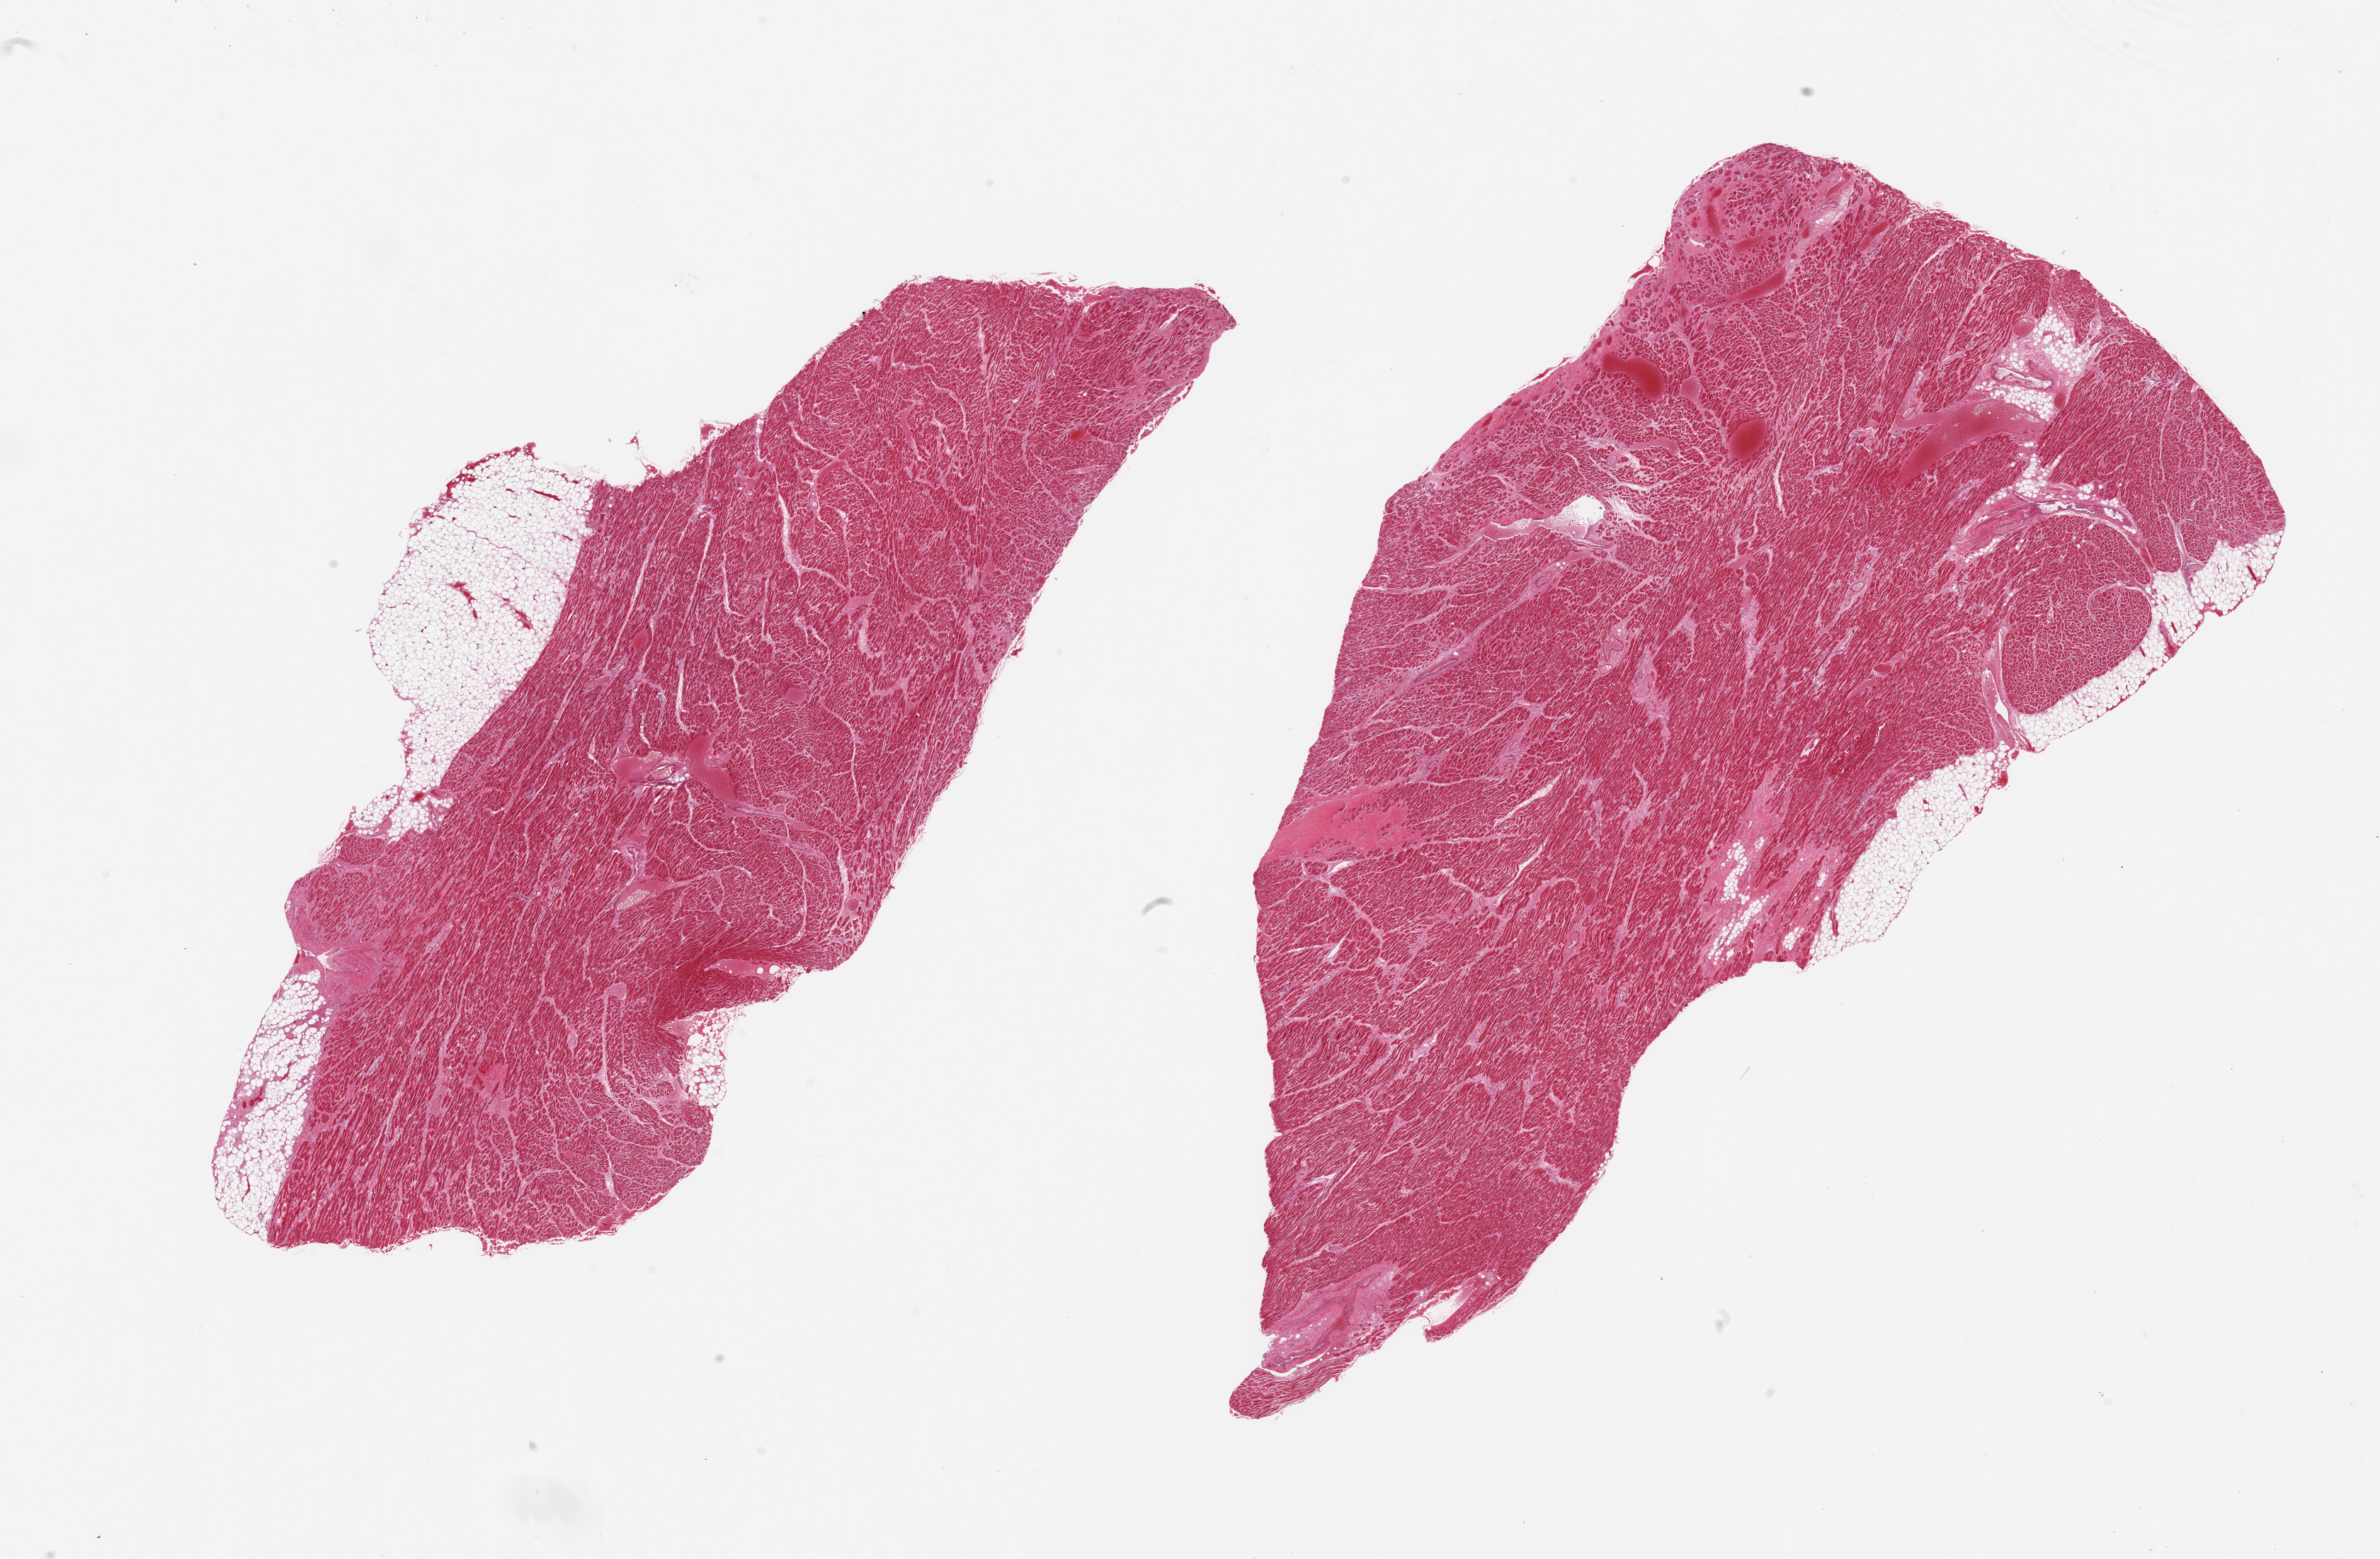
Whole-slide image, haematoxylin and eosin stain, shown as a low-resolution overview of the whole scanned area (about 26.6 x 17.4 mm); PAXgene-fixed, paraffin-embedded tissue; sampled site (target tissue): heart; donor tissue sample. Donor sex: male.
* review note (as recorded): 2 pieces; 5% patchy fibrosis; up to 1.5mm pericardial fat